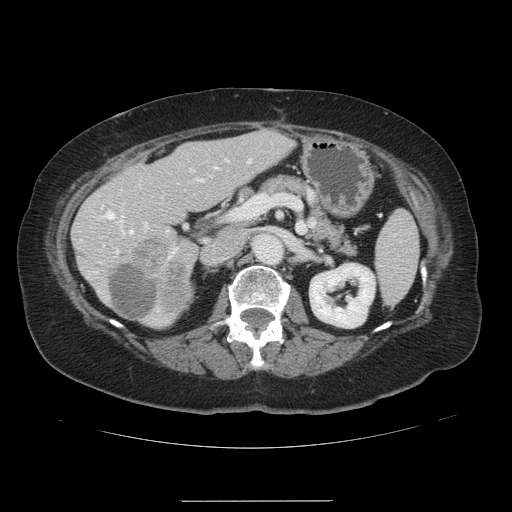
Contrast-enhanced abdominal CT, one axial slice. Position 63 of 141 along the scan axis. Intravenous contrast given. Soft-tissue window (W 400 / L 40 HU). 2.5 mm slice thickness. 512 × 512 image matrix, field of view 393 × 393 mm. Female patient, age 74 years. From the clinical record (not read from this slice): diagnosis: colorectal cancer liver metastases, imaged before liver resection; multiple liver metastases: yes; largest metastasis: 7 cm.
Structures marked on this image (outlined manually by an expert reader):
- hepatic veins: bounding box <103,183,142,235> (left, top, right, bottom; pixels)
- liver: <72,131,292,328>
- planned liver remnant (the part of the liver to remain after resection): <72,131,292,249>
- portal vein (with intrahepatic branches): <116,159,250,256>
- liver metastasis: <110,264,159,321>
- liver metastasis: <131,237,190,312>